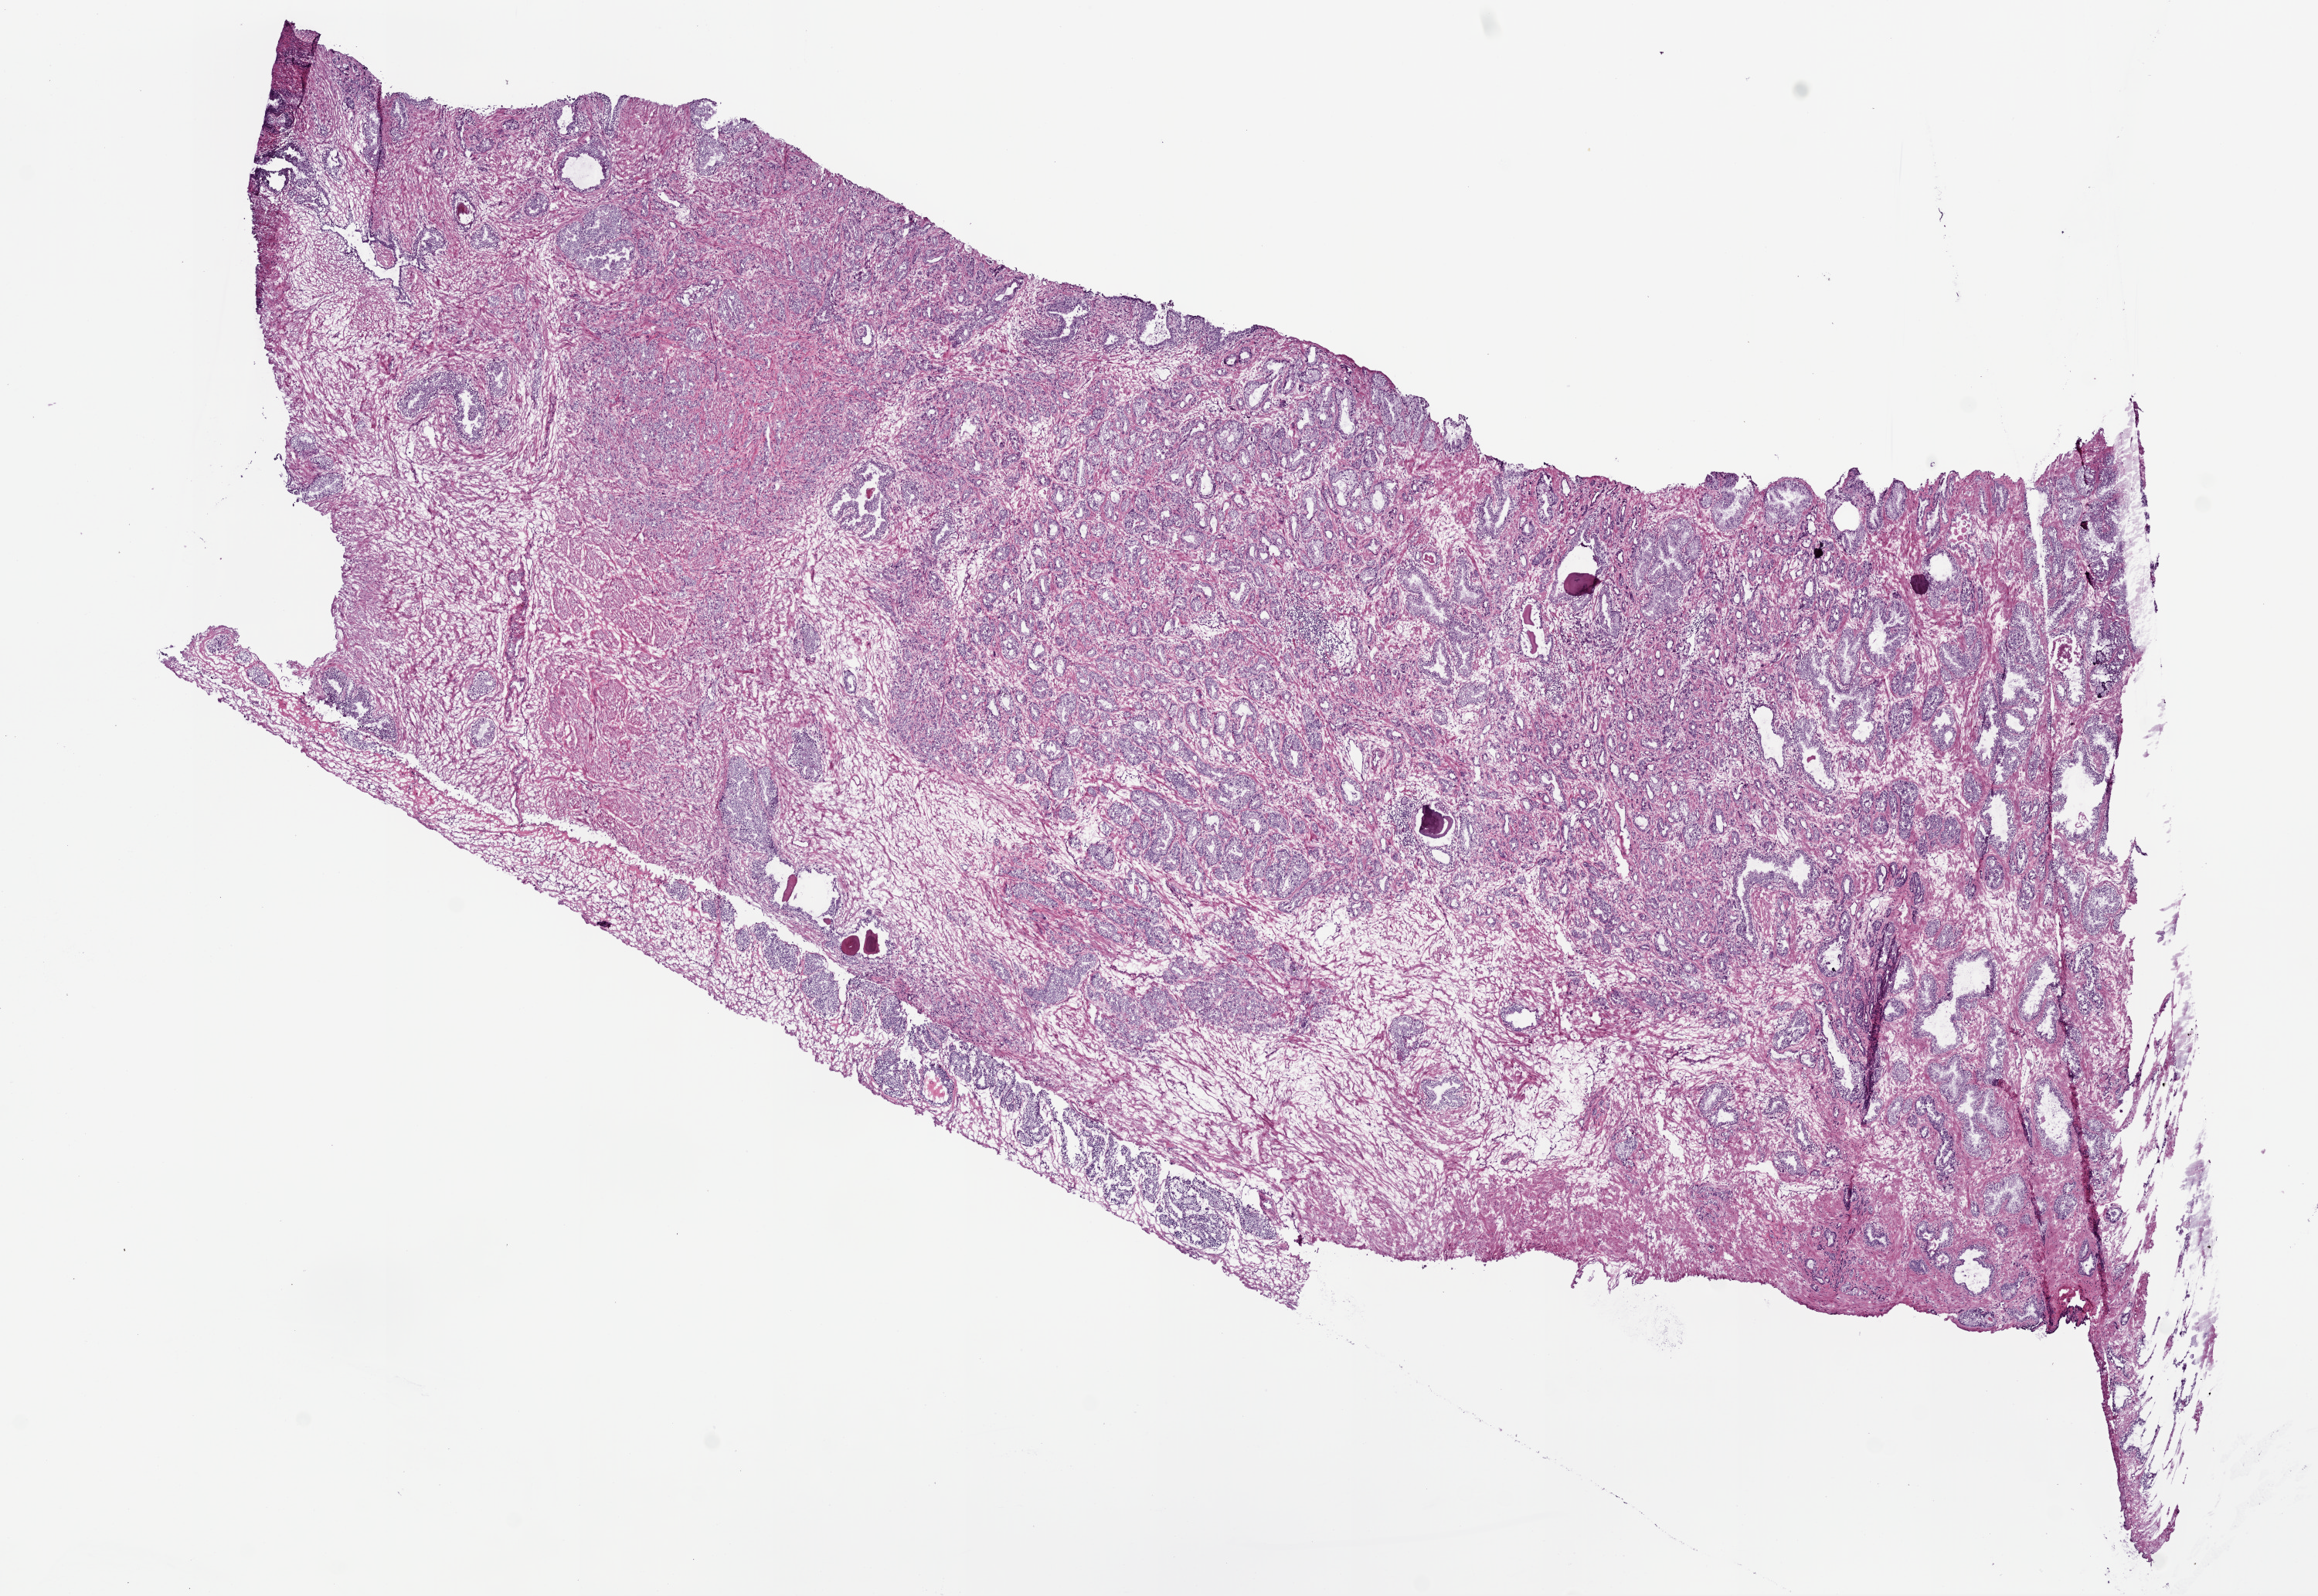
H&E whole-slide image — low-resolution overview of the scanned area, about 12.0 x 8.3 mm (slide scanned at 20x). Frozen section from the top of the tissue portion. Prostate, primary tumour sample. Male patient; age at initial diagnosis 56 years. Composition of this section per pathologist review: tumour cells 55%, tumour nuclei 60%.
Pathologic diagnosis: Acinar cell carcinoma.